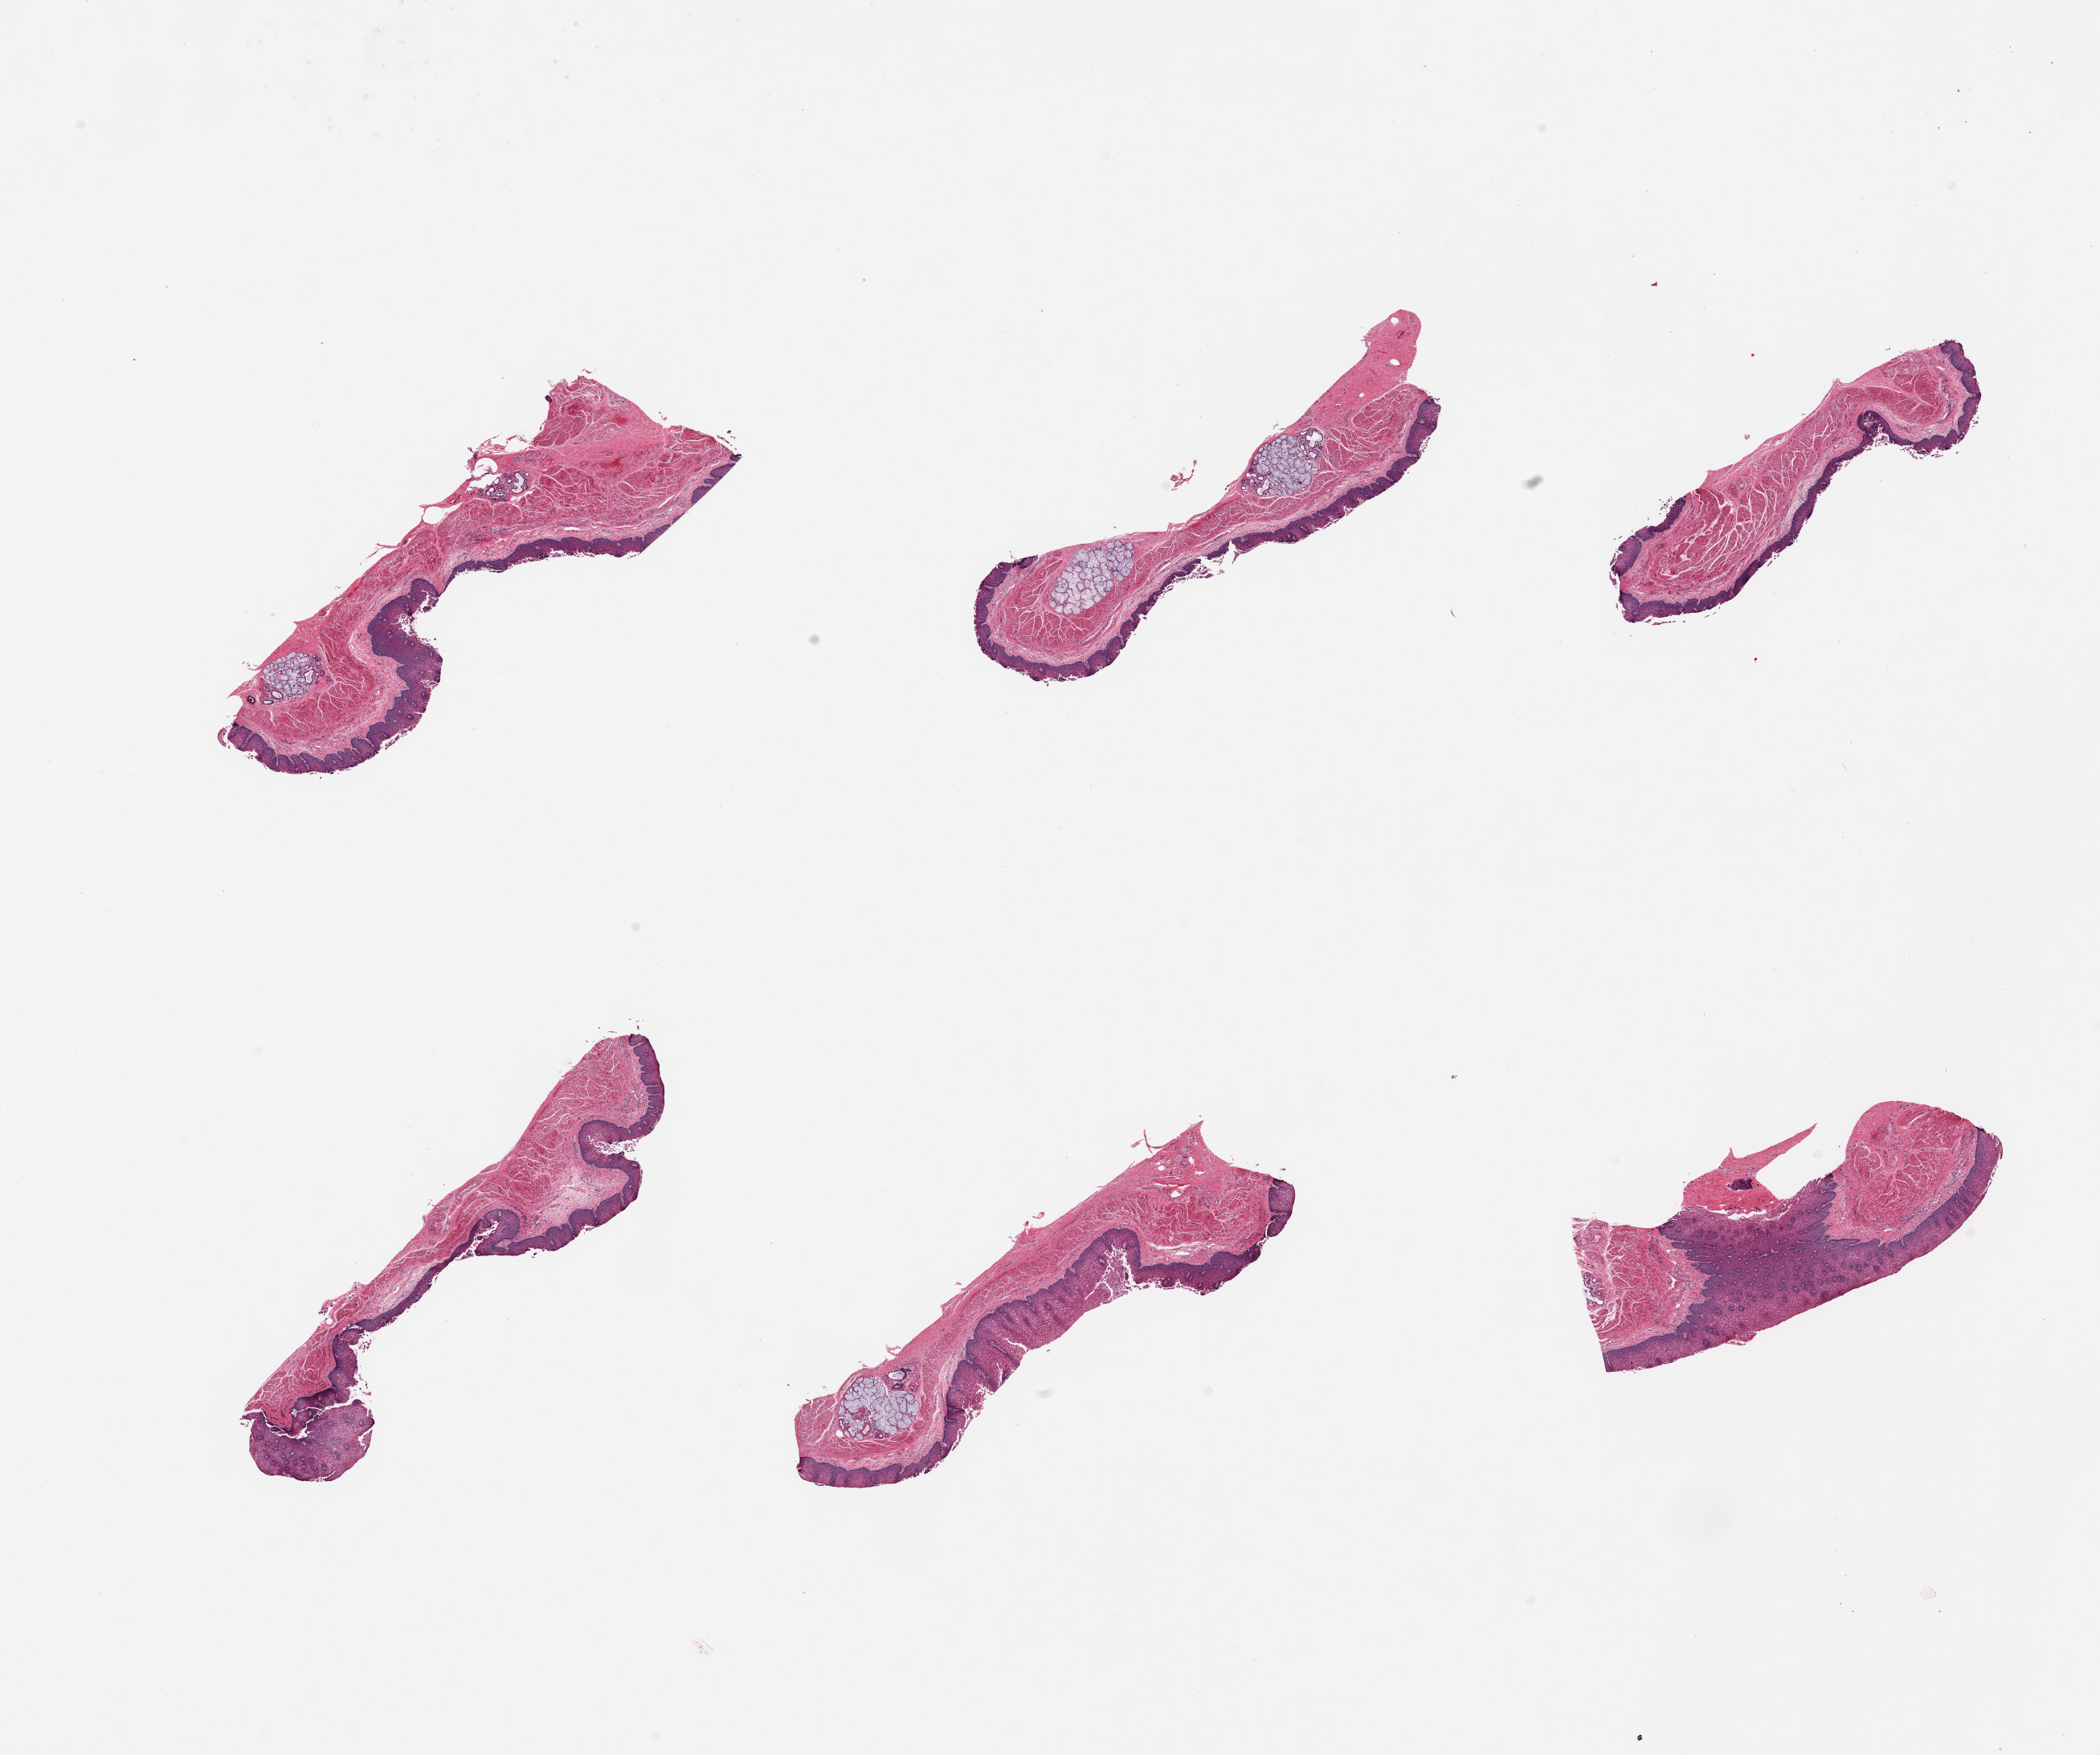
Hematoxylin and eosin (H&E) whole-slide image — whole scanned area (about 20.7 x 17.3 mm) shown as a low-resolution overview; PAXgene-fixed paraffin-embedded (PFPE) section; target tissue: esophageal mucous membrane; tissue donor sample. Male donor.
- review note (as recorded): 6 pieces, squamous mucosa 100-200 microns, 10-20% thickness; superficialy sloughing beginning; Submucosal mucus glands present